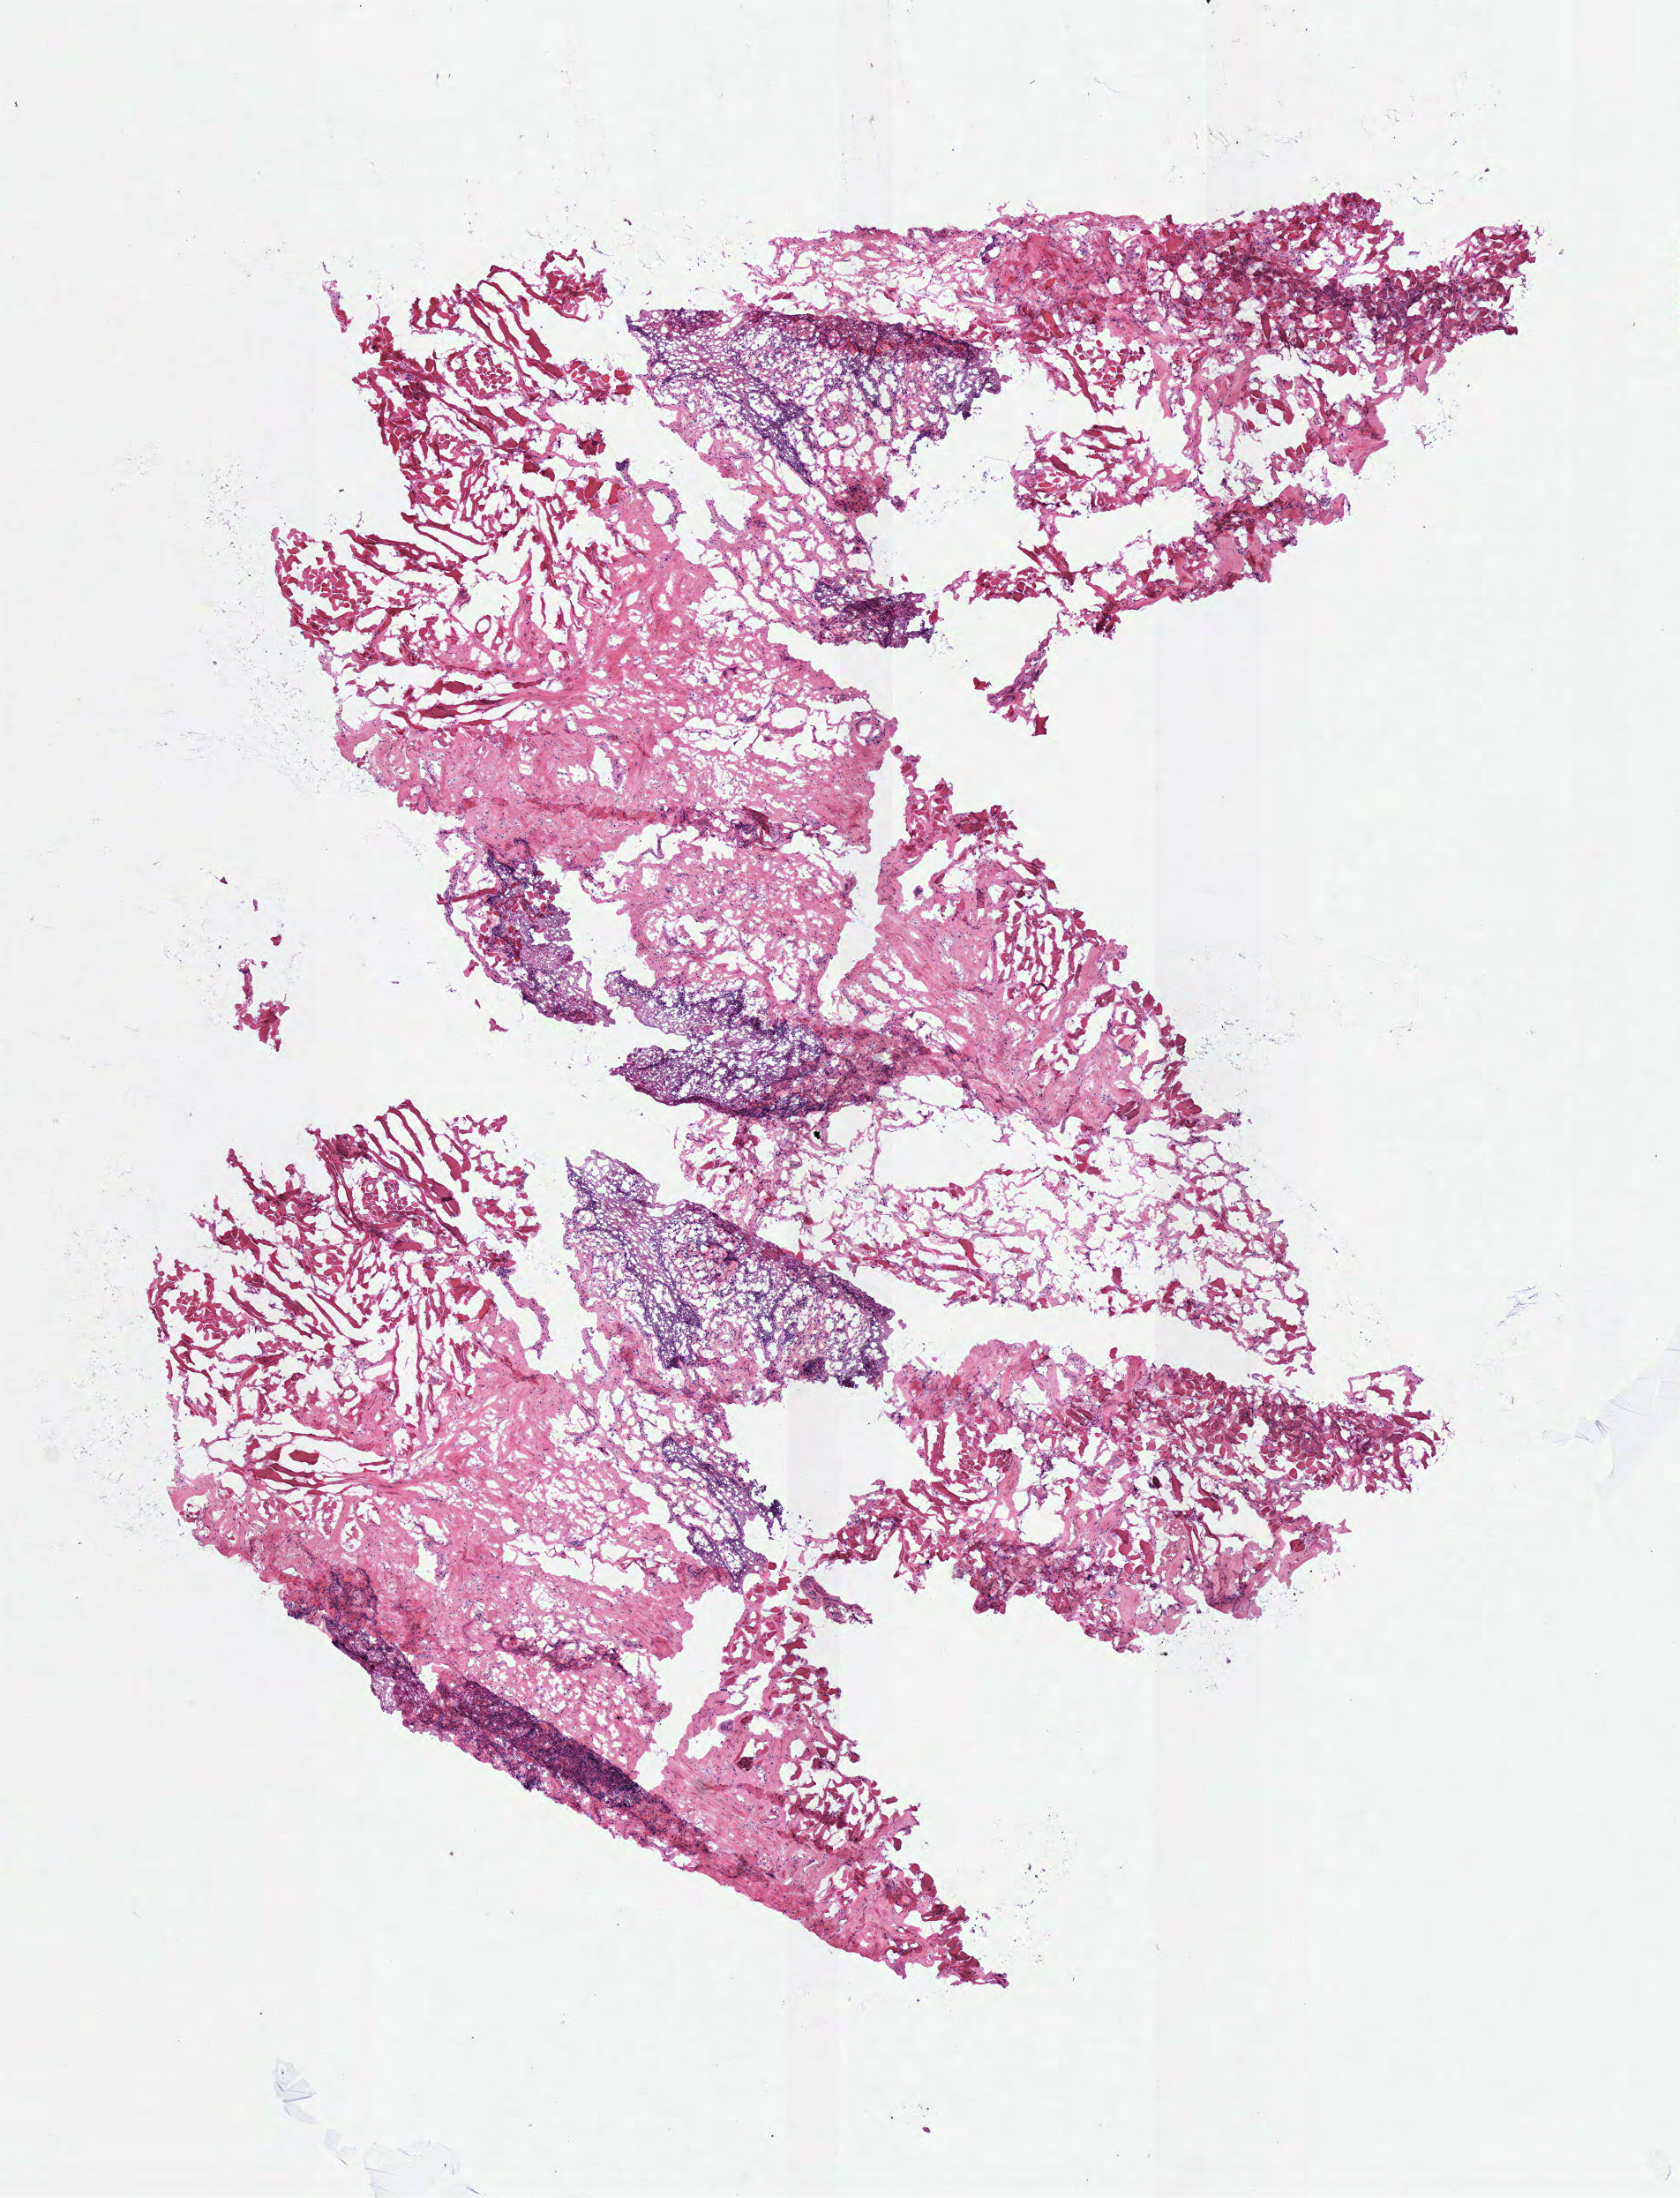
Digitized H&E tissue section (whole slide), a low-resolution overview of the entire scanned area, about 7.5 x 9.8 mm (slide scanned at 40x), frozen section, sample: solid tissue normal (non-tumour tissue), head and neck. Patient: female, age at initial diagnosis 65 years.
This section: solid tissue normal sample (biorepository sample class). Patient diagnosis: Squamous cell carcinoma, NOS (tongue, NOS).